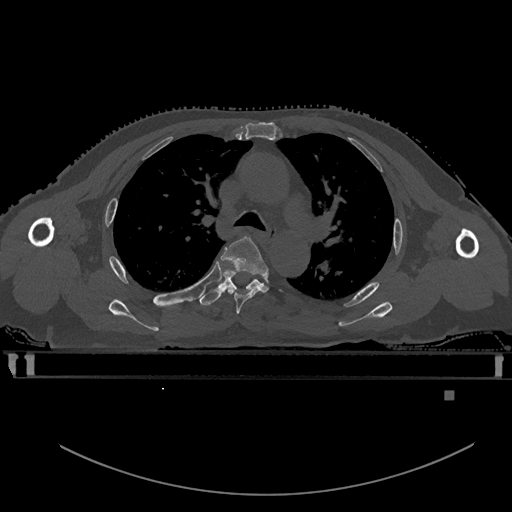
CT including the spine, one axial slice; slice 385 of 969 in the series (ordered by position); bone window (W 1800 / L 400 HU); 0.5 mm slice thickness; 512 × 512 image matrix, field of view 456 × 456 mm. Patient: male, 82 years. From the clinical record (not read from this slice): primary cancer: prostate; vertebrae with lytic lesions (as recorded): T11, T9, T8, T2.
Outlined on this slice (semi-automatic segmentation, software-assisted and operator-edited):
- T4 vertebra: bounding box <221,236,269,314> (left, top, right, bottom; pixels)
- T5 vertebra: <199,271,262,306>